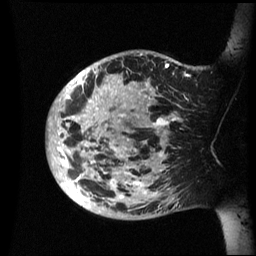
Breast MRI (dynamic contrast-enhanced), one sagittal slice; dynamic contrast-enhanced series, image 2 of 3 at this slice position (ordered by acquisition); 1.5 T; TE 4.2 ms, TR 8.4 ms; 256 × 256 image matrix, field of view 230 × 230 mm. Female patient, age 48 years.
Annotated regions visible in this slice (semi-automatic segmentation, software-assisted and operator-edited):
- analysis volume of interest (the breast-tissue region the enhancement analysis was run in; not a lesion): bounding box <47,50,202,220> (left, top, right, bottom; pixels)
- tumour enhancement mask (voxels above the 70 % enhancement threshold inside the analysis volume of interest): <47,54,187,206>